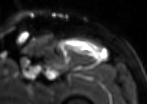
MRI of an extremity soft-tissue mass, one axial slice; slice 77 of 85 in the series (ordered by position); T2-weighted fat-saturated; MR volume resampled by the dataset authors to the PET/CT grid (not the native acquisition matrix); 3.27 mm slice thickness; 147 × 104 image matrix, field of view 144 × 102 mm. Male patient. From the clinical record (not read from this slice): histological type: extraskeletal osteosarcoma; grade: high; site of the primary tumour: thigh.
Annotated regions visible in this slice (expert contour drawn on MRI and transferred to this co-registered scan by the dataset authors):
- gross tumour volume (mass): bounding box <65,37,105,59> (left, top, right, bottom; pixels)